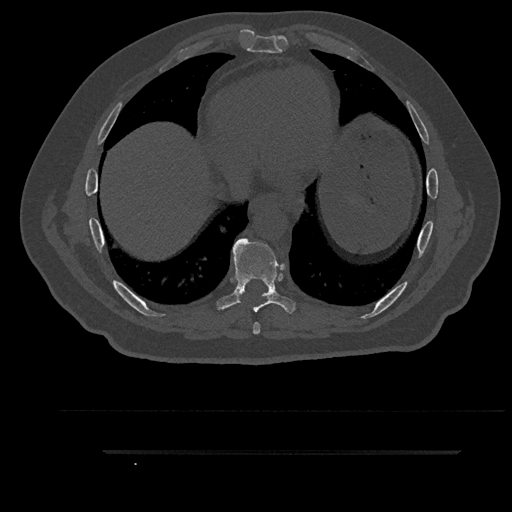
CT including the spine, one axial slice. Slice 480 of 797 in the series (ordered by position). Reconstruction kernel Br40s/3. Bone window (W 1800 / L 400 HU). 512 × 512 image matrix, field of view 432 × 432 mm. Patient: male, 63 years. Case-level facts recorded for this patient, not image findings: primary cancer: renal; vertebrae with lytic lesions (as recorded): T8.
Annotated regions visible in this slice (semi-automatically segmented with operator editing):
- T7 vertebra: bounding box (x1, y1, x2, y2) in pixels: (253, 322, 260, 334)
- T8 vertebra: (215, 238, 297, 315)